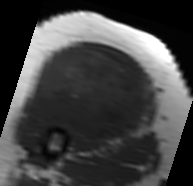
MRI of an extremity soft-tissue mass, one axial slice. MR volume resampled by the dataset authors to the PET/CT grid (not the native acquisition matrix). 193 × 186 image matrix, field of view 188 × 182 mm. Female patient. Case-level facts recorded for this patient, not image findings: histological type: malignant solitary fibrous tumor; grade: intermediate; site of the primary tumour: right thigh.
Annotated regions visible in this slice (expert contour drawn on MRI and transferred to this co-registered scan by the dataset authors):
- gross tumour volume including surrounding oedema: box from (x=22, y=46) to (x=153, y=143) px
- gross tumour volume (mass): (x=29, y=46)–(x=148, y=141)